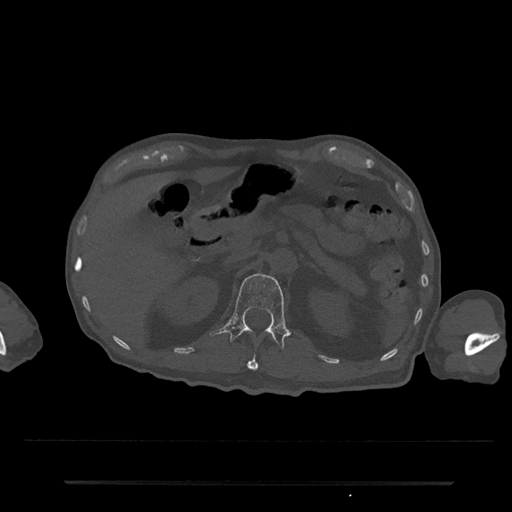
CT including the spine, one axial slice. Slice 146 of 797 in the series (ordered by position). Bone window (W 1800 / L 400 HU). 0.5 mm slice thickness. 512 × 512 image matrix. Patient: male, 74 years. From the clinical record (not read from this slice): primary cancer: prostate.
Structures marked on this image (semi-automatically segmented with operator editing):
- L1 vertebra: bounding box (x1, y1, x2, y2) in pixels: (211, 273, 289, 350)
- T12 vertebra: (247, 356, 258, 371)